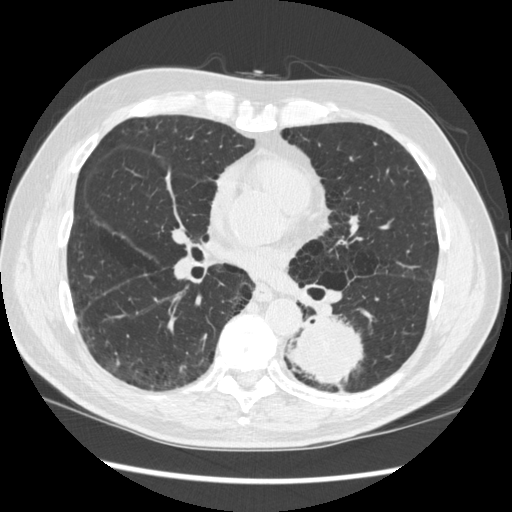
Low-dose screening chest CT, one axial slice; position 158 of 348 along the scan axis; reconstruction kernel STANDARD; 120 kVp; lung window (W 1500 / L -600 HU); 512 × 512 image matrix, field of view 360 × 360 mm.
Outlined on this slice (manually delineated by an expert):
- lesion 1 (tumor, lower lobe of left lung): bounding box <289,317,363,385> (left, top, right, bottom; pixels)